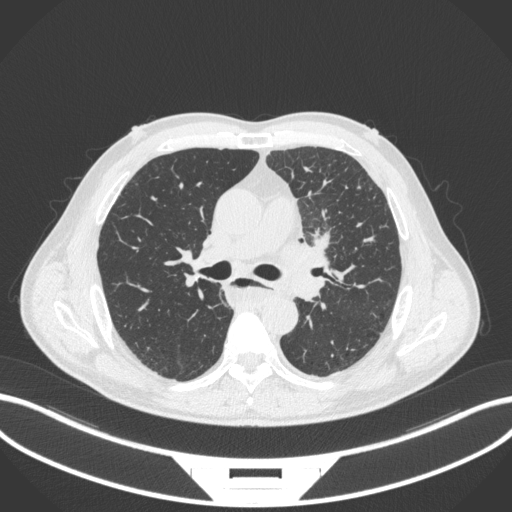
Chest CT, one axial slice. Lung window (W 1500 / L -600 HU). 1 mm slice thickness. 512 × 512 image matrix, field of view 400 × 400 mm. Patient: male, 57 years. From the clinical record (not read from this slice): clinical TNM (as recorded): T2a N1 M0.
Outlined on this slice (rectangle marked by the reading radiologist):
- lung tumour (recorded histology: squamous cell carcinoma): box from (x=275, y=228) to (x=340, y=279) px